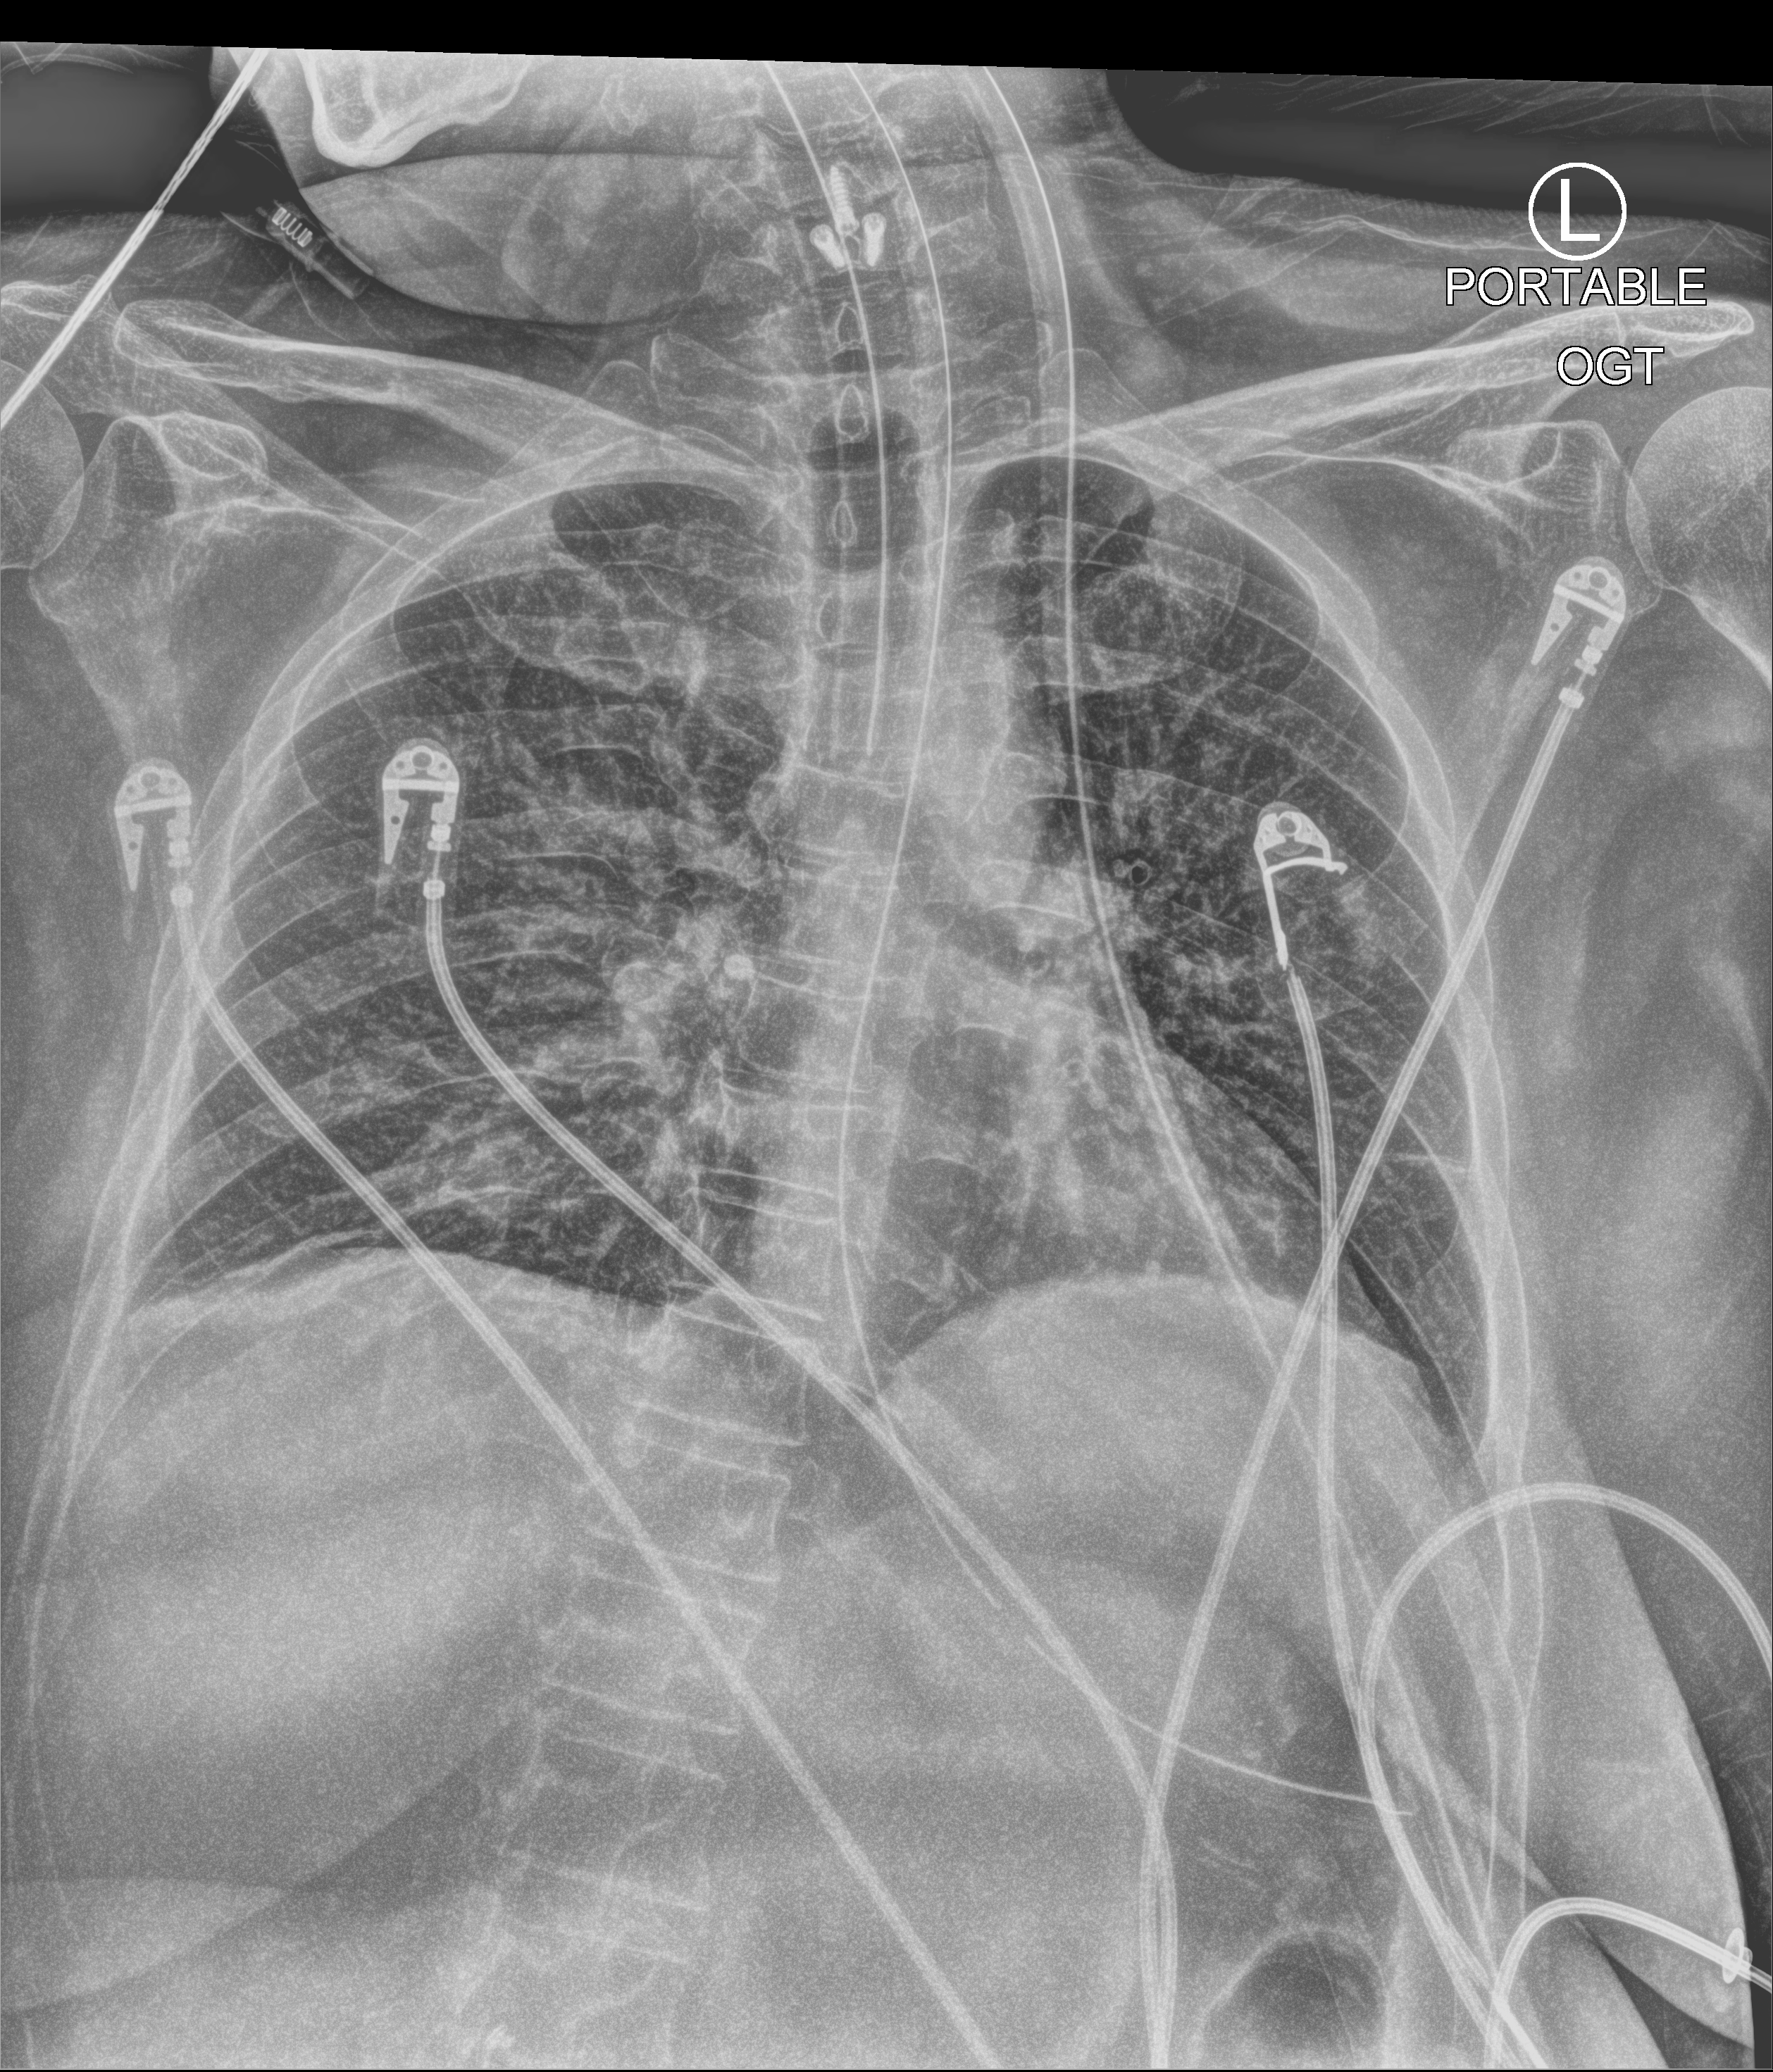
Bedside chest radiograph (computed radiography), anteroposterior (AP) projection. Female patient hospitalised with COVID-19, age 18–59 years.
From the hospital-stay record, not from the radiograph (when in the stay this image was taken is not recorded): length of hospital stay: 44 days; mechanically ventilated during this hospital stay: no; admitted to intensive care during this hospital stay: yes.